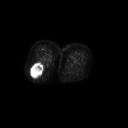
FDG PET of an extremity soft-tissue mass (from a PET/CT study), one axial slice; slice 33 of 267 in the series (ordered by position); 3.27 mm slice thickness; 128 × 128 image matrix, field of view 700 × 700 mm. Patient: female, 70 years. From the clinical record (not read from this slice): histological type: synovial sarcoma; grade: intermediate; site of the primary tumour: right buttock.
Outlined on this slice (expert contour drawn on MRI and transferred to this co-registered scan by the dataset authors):
- gross tumour volume including surrounding oedema: box from (x=30, y=61) to (x=43, y=77) px
- gross tumour volume (mass): (x=31, y=62)–(x=43, y=77)